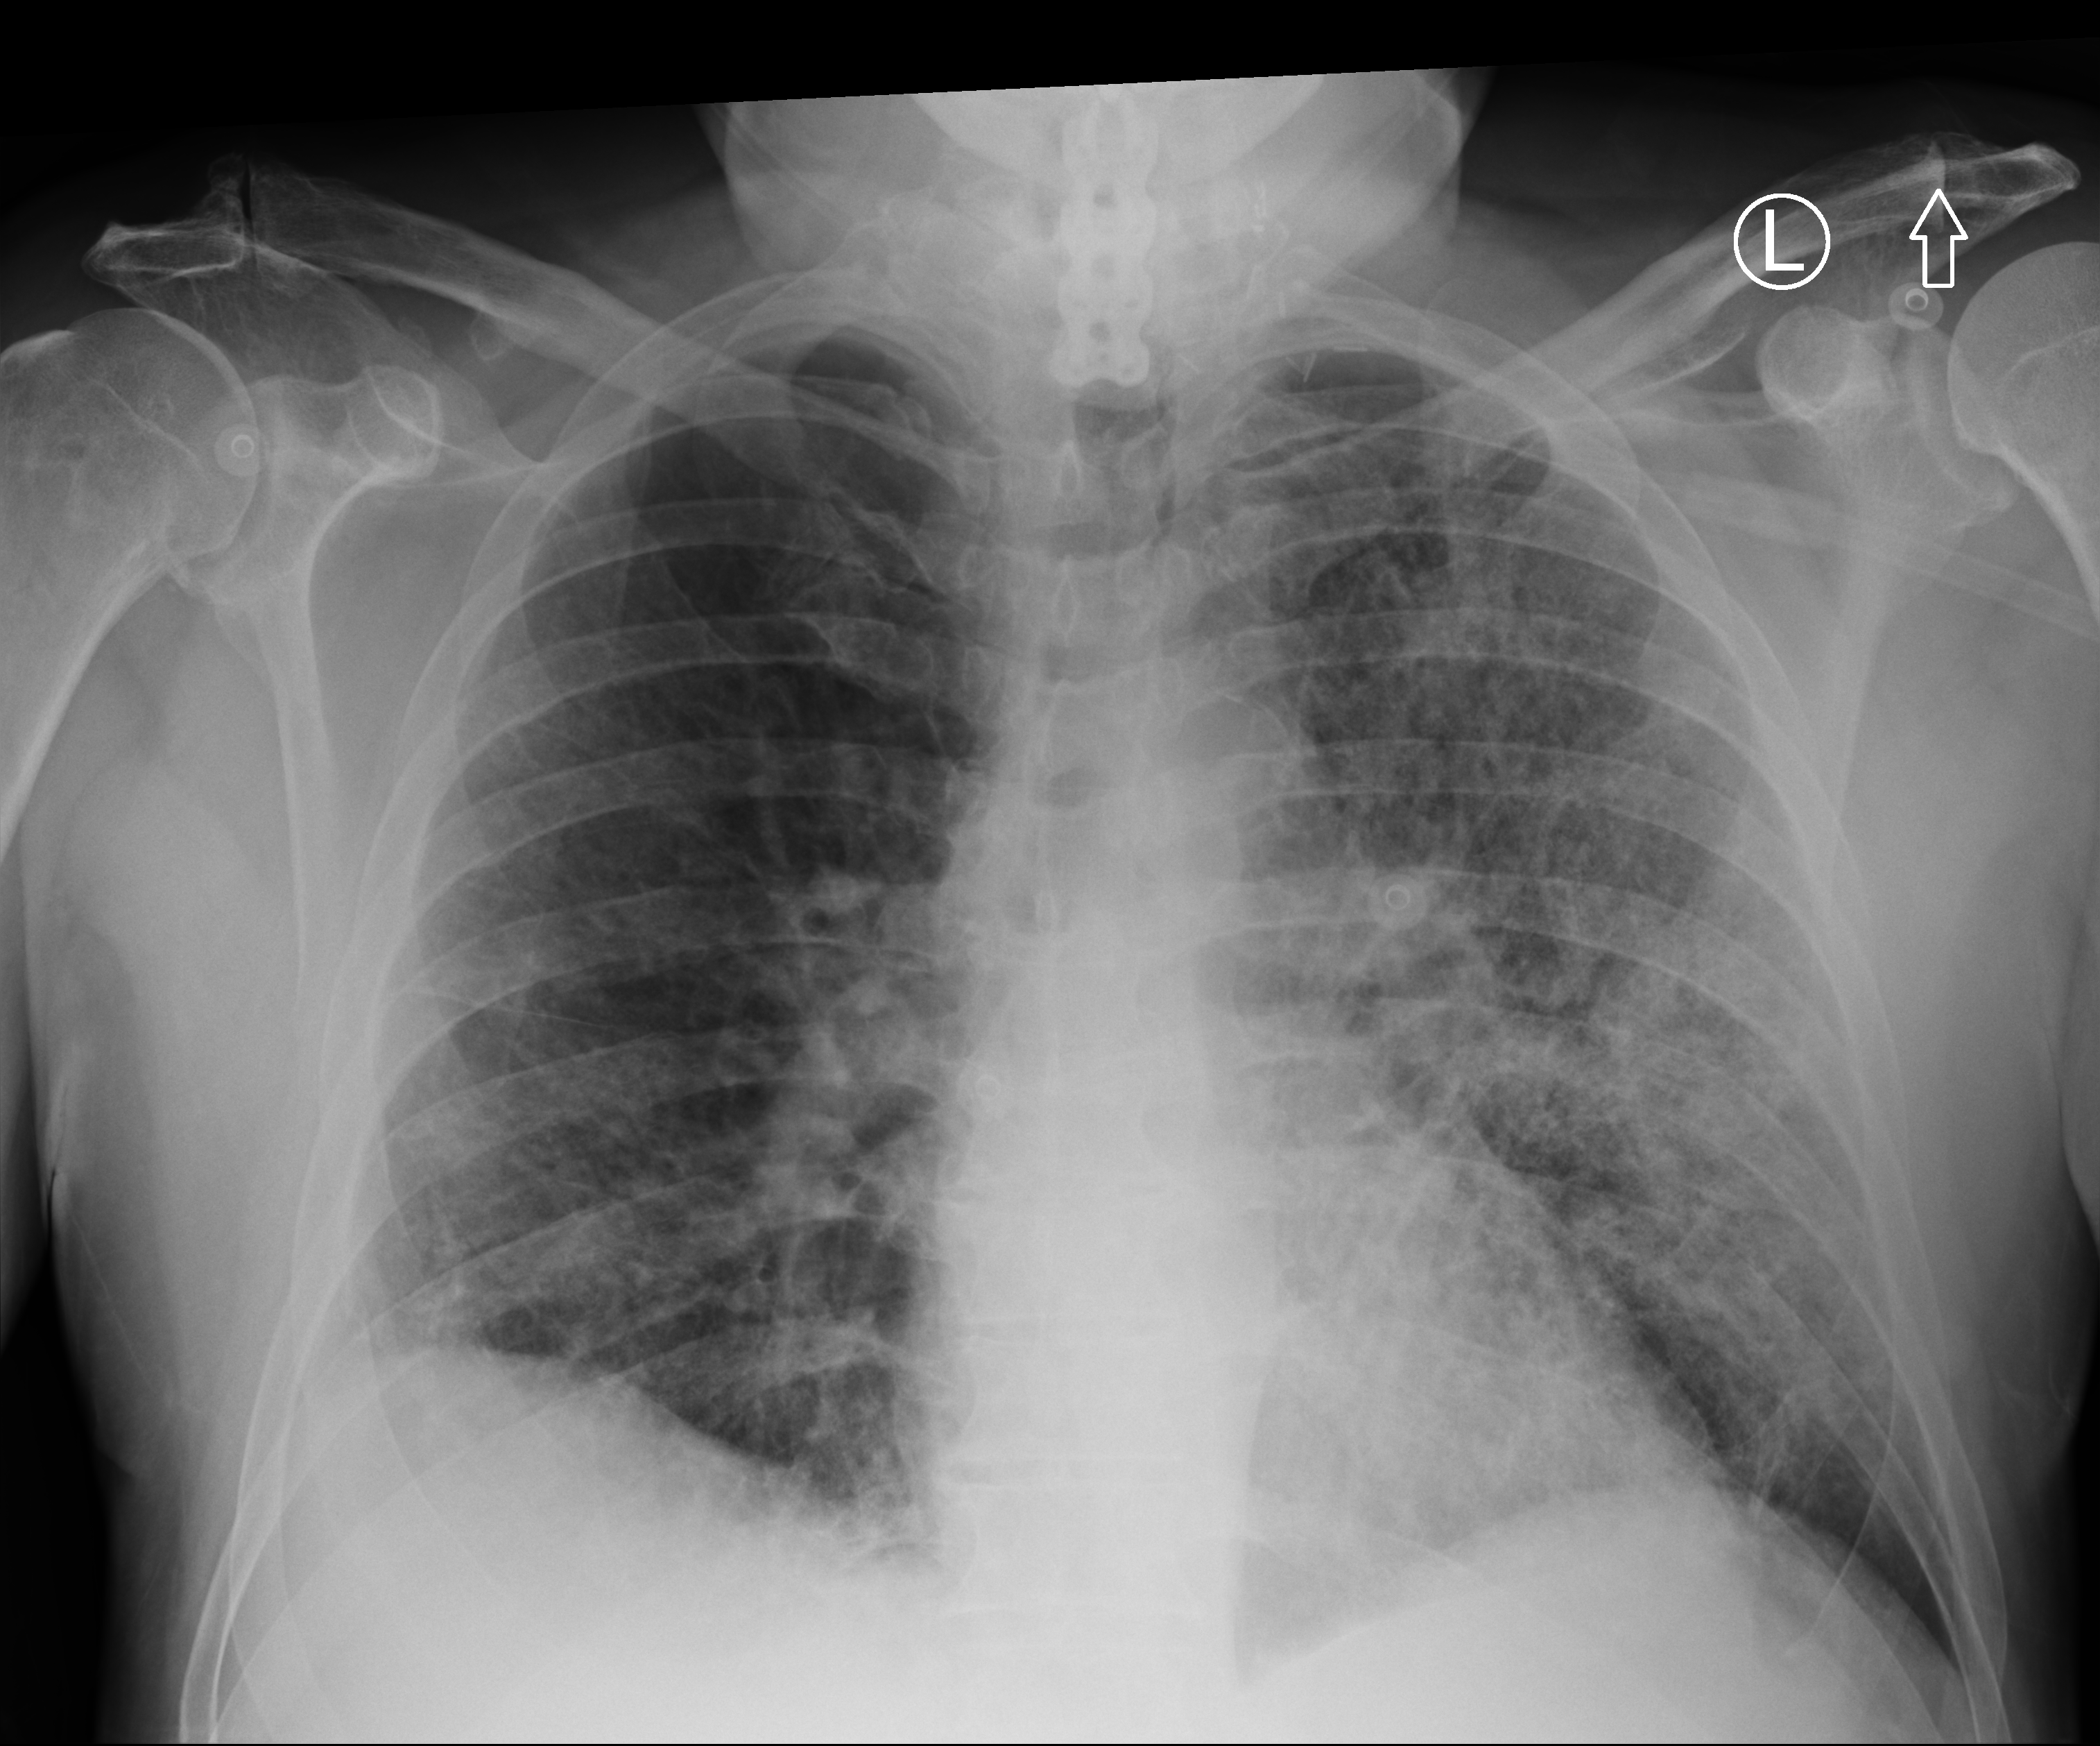
Chest X-ray (portable), anteroposterior (AP) projection. Male patient hospitalised with COVID-19, age 60–74 years.
From the hospital-stay record, not from the radiograph (when in the stay this image was taken is not recorded): admitted to intensive care during this hospital stay: yes; mechanically ventilated during this hospital stay: yes.